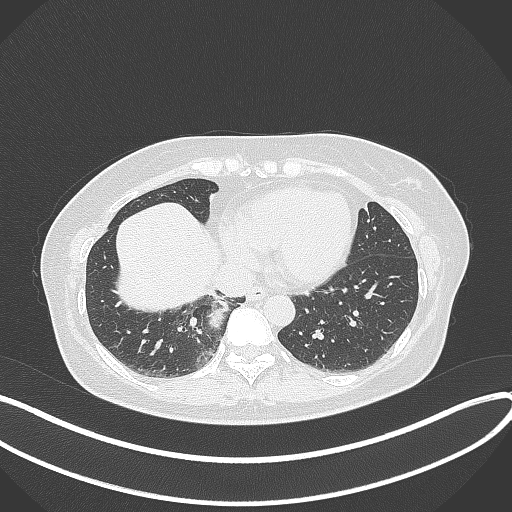
Chest CT, one axial slice. Position 103 of 331 along the scan axis. 120 kVp. Lung window (W 1500 / L -600 HU). 1 mm slice thickness. 512 × 512 image matrix. Patient: female, 54 years. From the clinical record (not read from this slice): clinical TNM (as recorded): T4 N0 M0.
Annotated regions visible in this slice (bounding box drawn by a radiologist):
- lung tumour (recorded histology: adenocarcinoma): bounding box <202,298,226,330> (left, top, right, bottom; pixels)